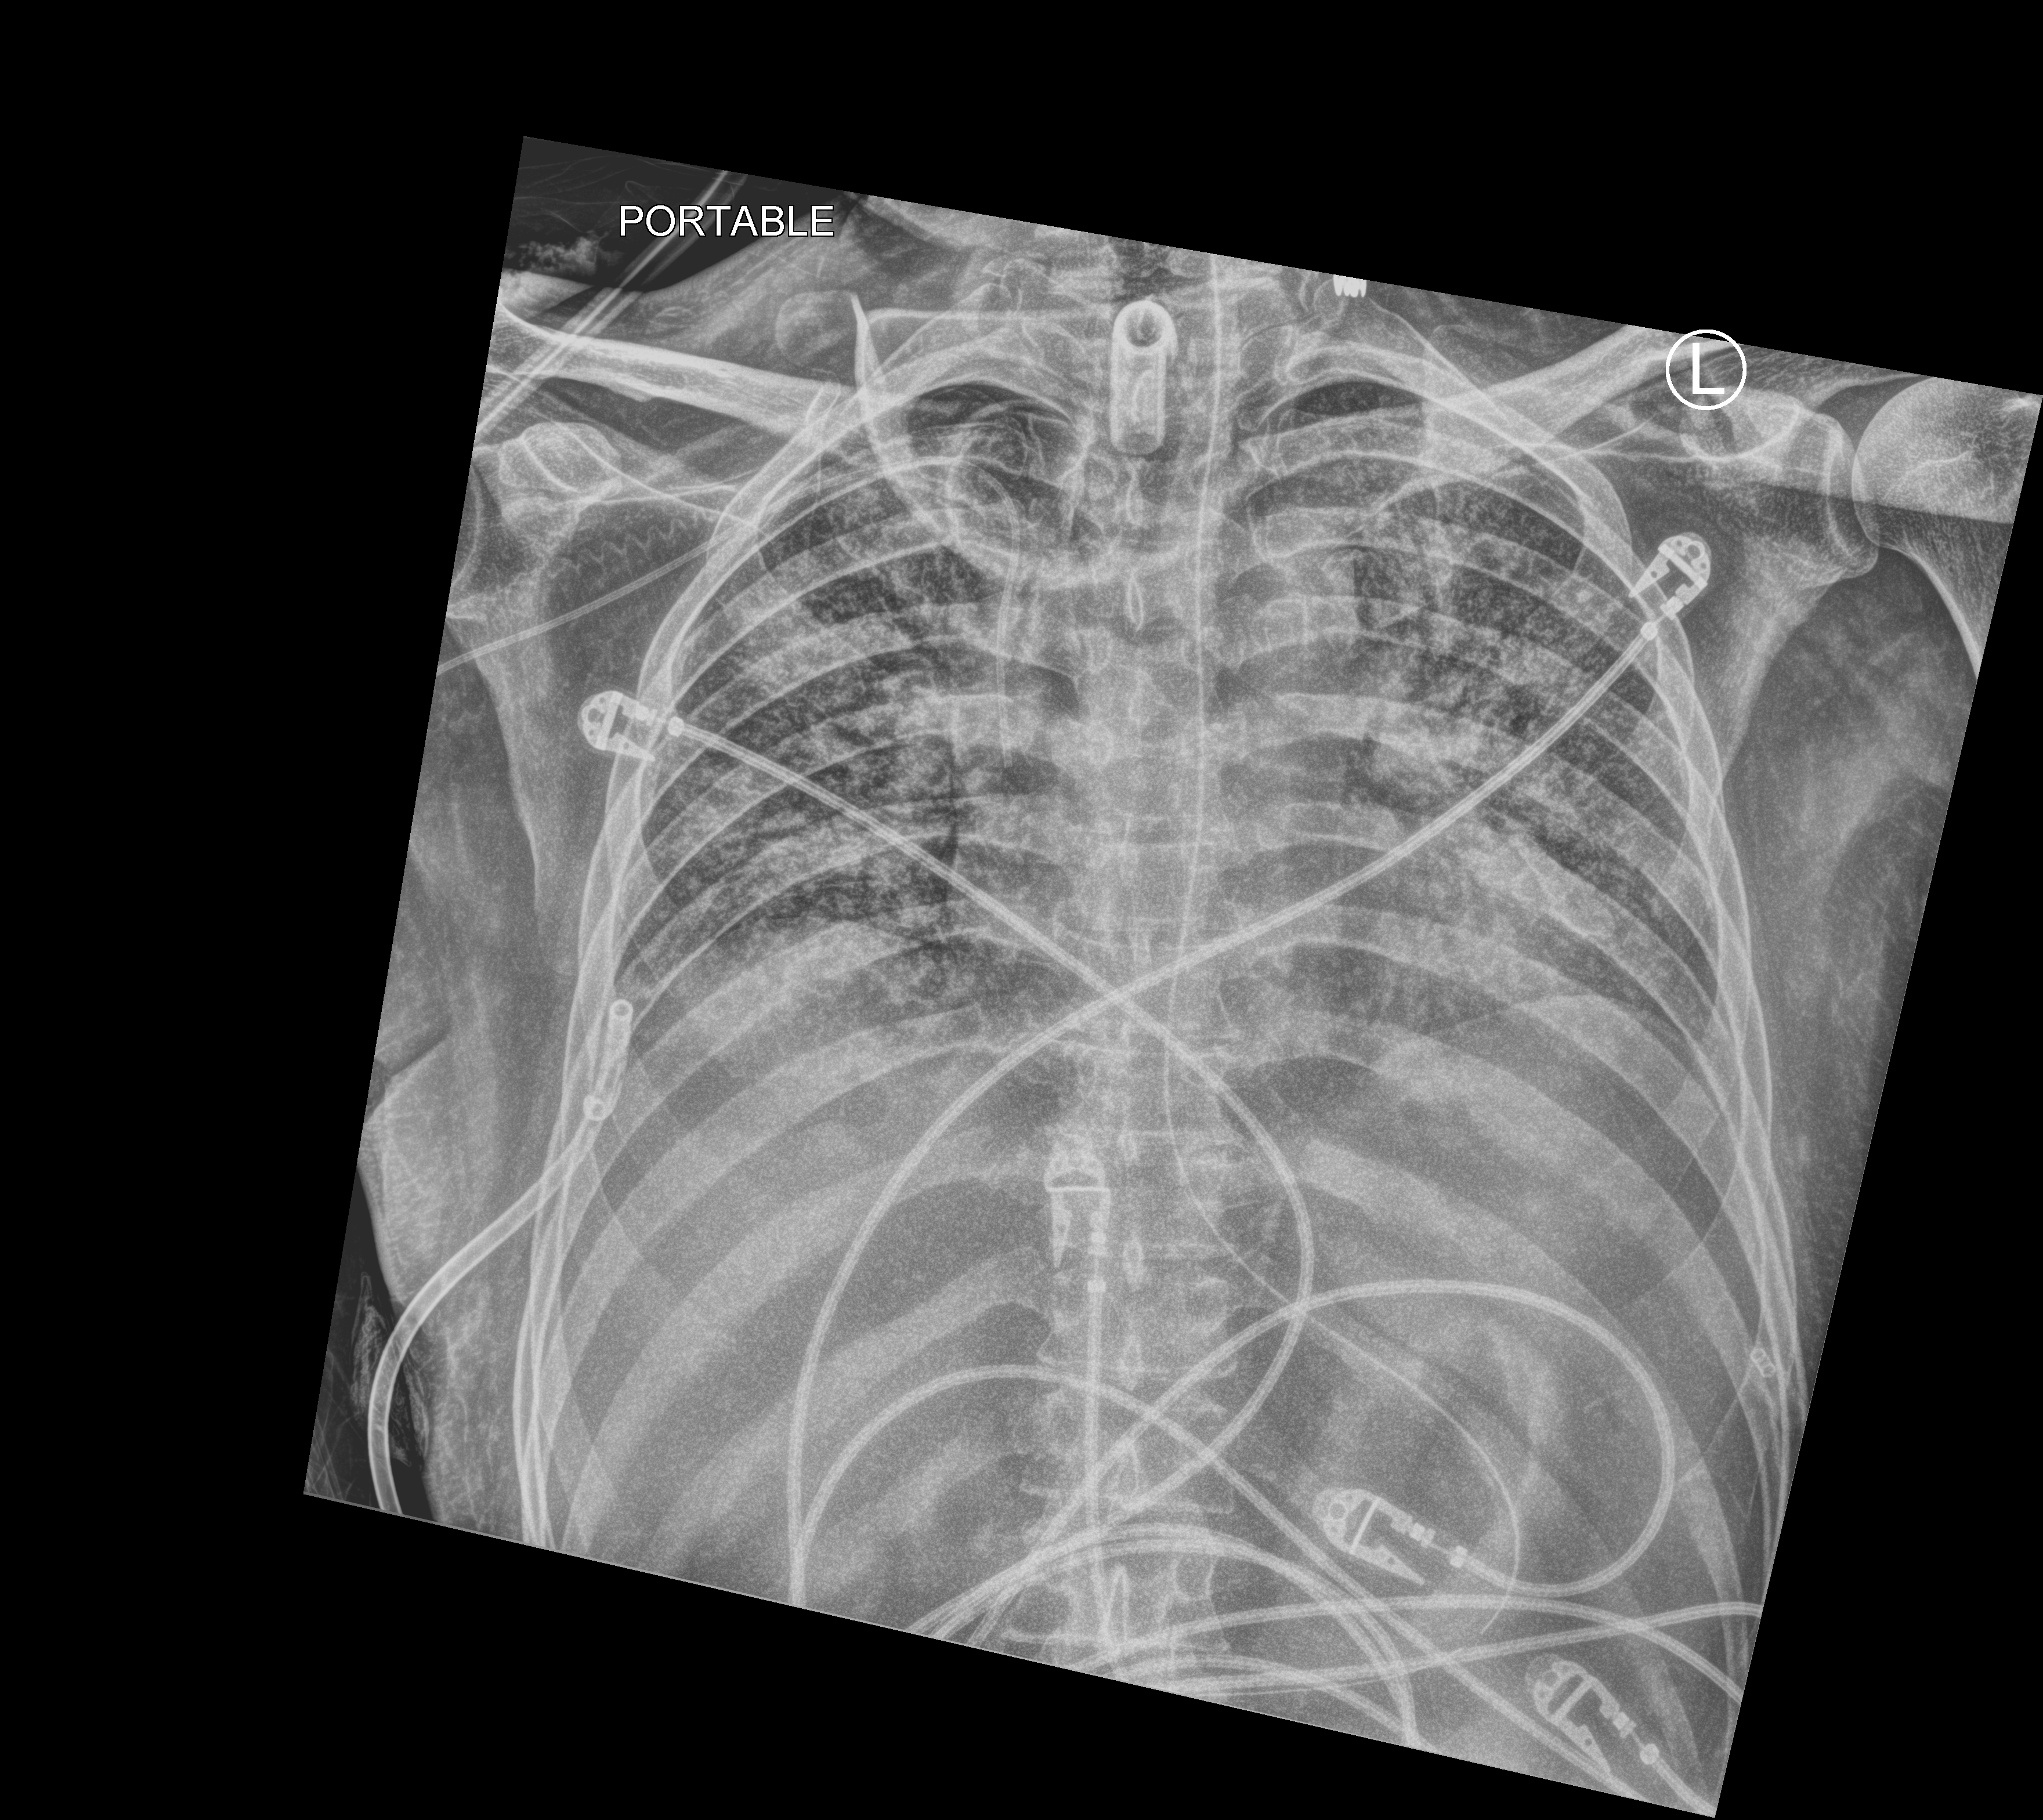
Bedside chest radiograph (computed radiography); anteroposterior (AP) projection. Patient hospitalised with COVID-19; male, aged 18–59 years.
Hospital-stay facts (about this admission, not read from this image; timing relative to this image not recorded): mechanically ventilated during this hospital stay: yes; admitted to intensive care during this hospital stay: yes; chronic kidney disease (admission record): no.